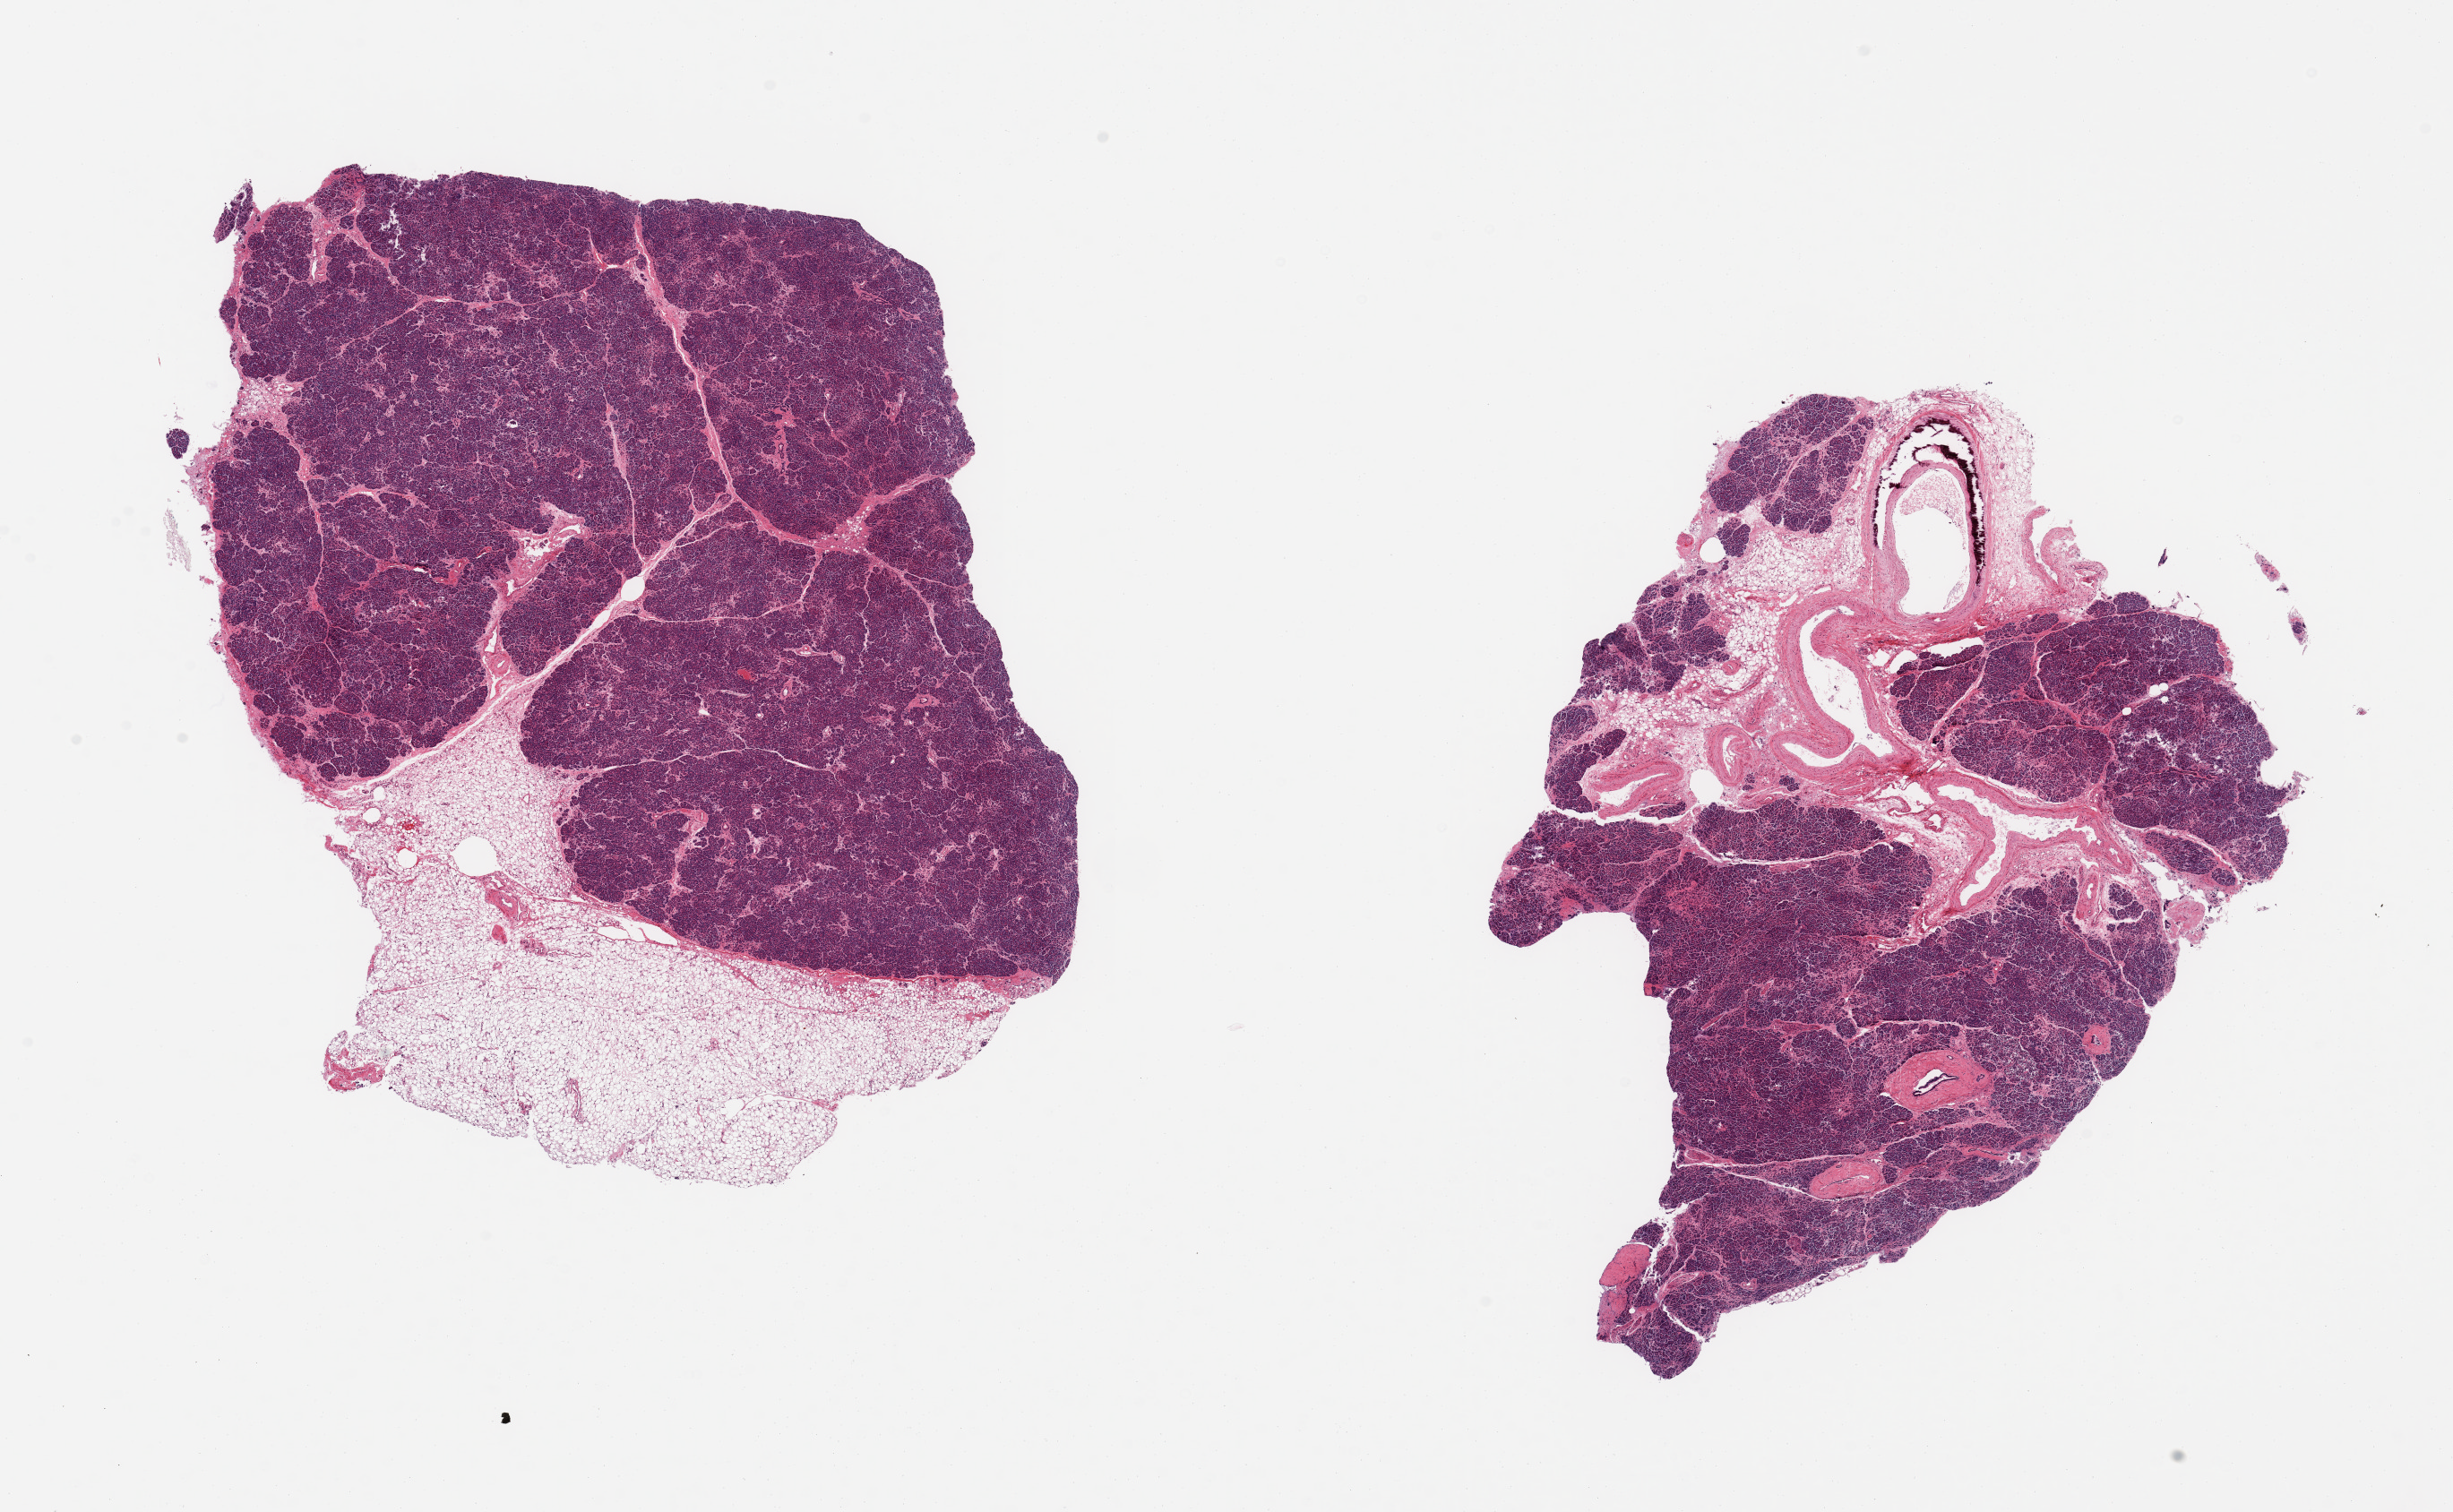
Digitized haematoxylin and eosin-stained section, brightfield — whole scanned area (about 21.7 x 13.4 mm) shown as a low-resolution overview; PAXgene-fixed, paraffin-embedded tissue; target tissue: pancreas; donor tissue sample.
Review note (as recorded): 2 pieces; 1 piece has 30% external fat; other has 30% large blood vessels & fat.